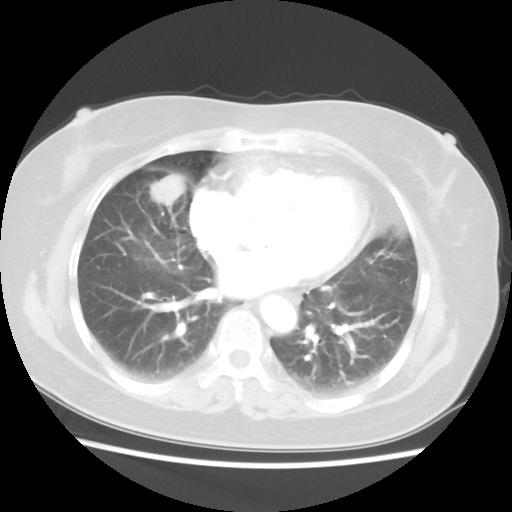
Chest CT, one axial slice. Slice 20 of 48 in the series (ordered by position). 100 kVp. Lung window (W 1500 / L -600 HU). 5 mm slice thickness. 512 × 512 image matrix, field of view 343 × 343 mm. Patient: female, 61 years. Case-level facts recorded for this patient, not image findings: clinical TNM (as recorded): T1c N0 M0.
Outlined on this slice (bounding box drawn by a radiologist):
- lung tumour (recorded histology: adenocarcinoma): bounding box (x1, y1, x2, y2) in pixels: (148, 173, 186, 209)